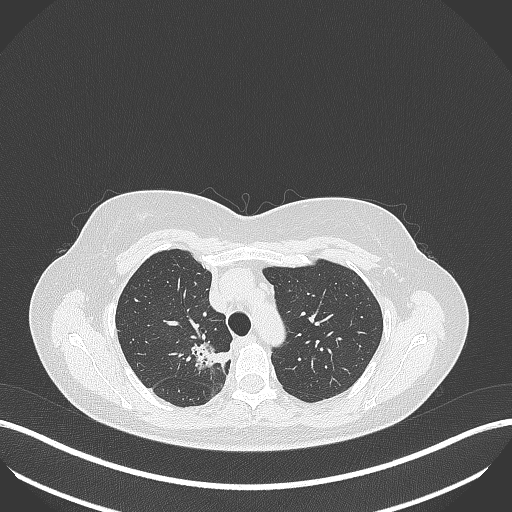
Chest CT, one axial slice. Position 297 of 386 along the scan axis. Reconstruction kernel B70f. 120 kVp. Lung window (W 1500 / L -600 HU). 1 mm slice thickness. 512 × 512 image matrix. Patient: female, 65 years. From the clinical record (not read from this slice): clinical TNM (as recorded): T1b N0 M0; histopathological grade: G2.
Structures marked on this image (rectangle marked by the reading radiologist):
- lung tumour (recorded histology: adenocarcinoma): bounding box (x1, y1, x2, y2) in pixels: (187, 338, 233, 376)